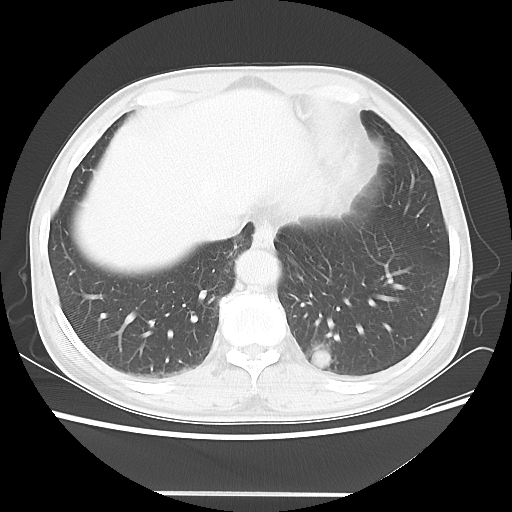
Chest CT, one axial slice. Position 13 of 60 along the scan axis. 100 kVp. Lung window (W 1500 / L -600 HU). 5 mm slice thickness. 512 × 512 image matrix, field of view 360 × 360 mm. Patient: male, 55 years. From the clinical record (not read from this slice): clinical TNM (as recorded): T1c N3 M0; histopathological grade: G3.
Annotated regions visible in this slice (bounding box drawn by a radiologist):
- lung tumour (recorded histology: small cell carcinoma): bounding box (x1, y1, x2, y2) in pixels: (308, 344, 345, 377)